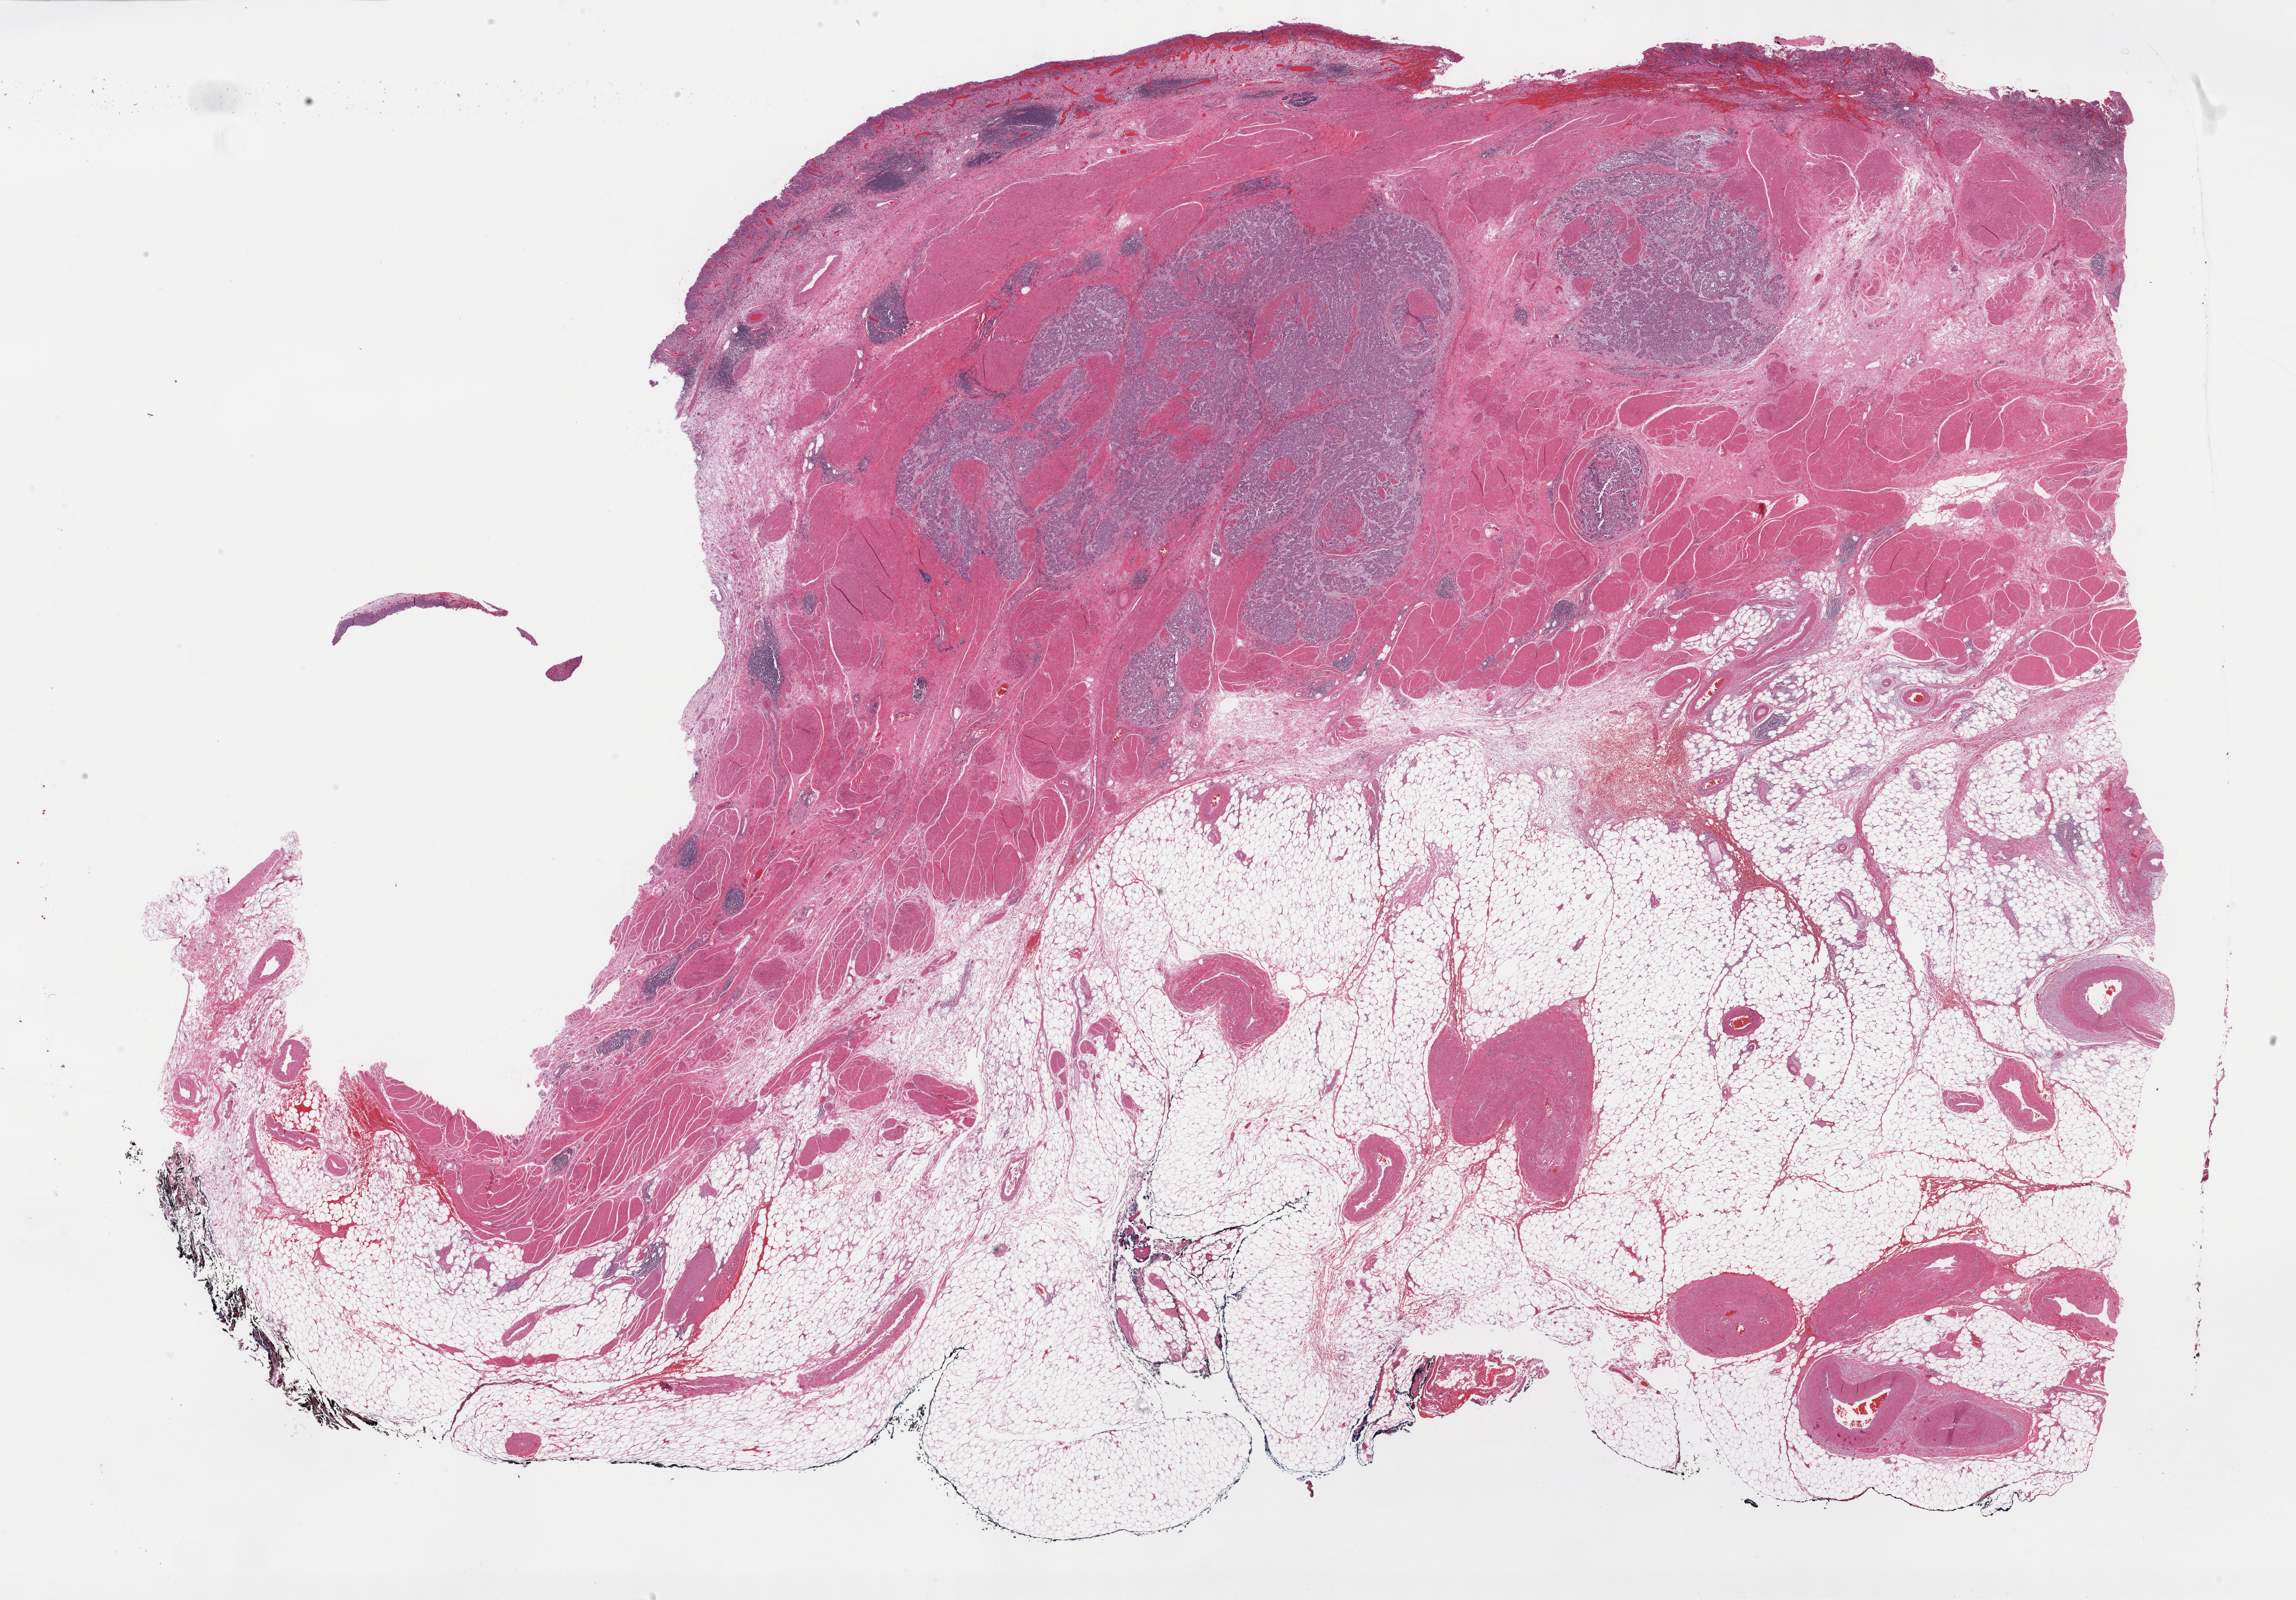
Whole-slide histology image, H&E, whole scanned area (about 31.7 x 22.1 mm, slide scanned at 40x) shown as a low-resolution overview. Formalin-fixed paraffin-embedded (FFPE) diagnostic section. Bladder, primary tumour sample. Male patient; age at initial diagnosis 61 years. Histologic grade: high grade.
Lymph nodes positive (case pathology): 5 of 24 examined. AJCC pathologic stage: IV. Diagnosis: Transitional cell carcinoma (posterior wall of bladder).